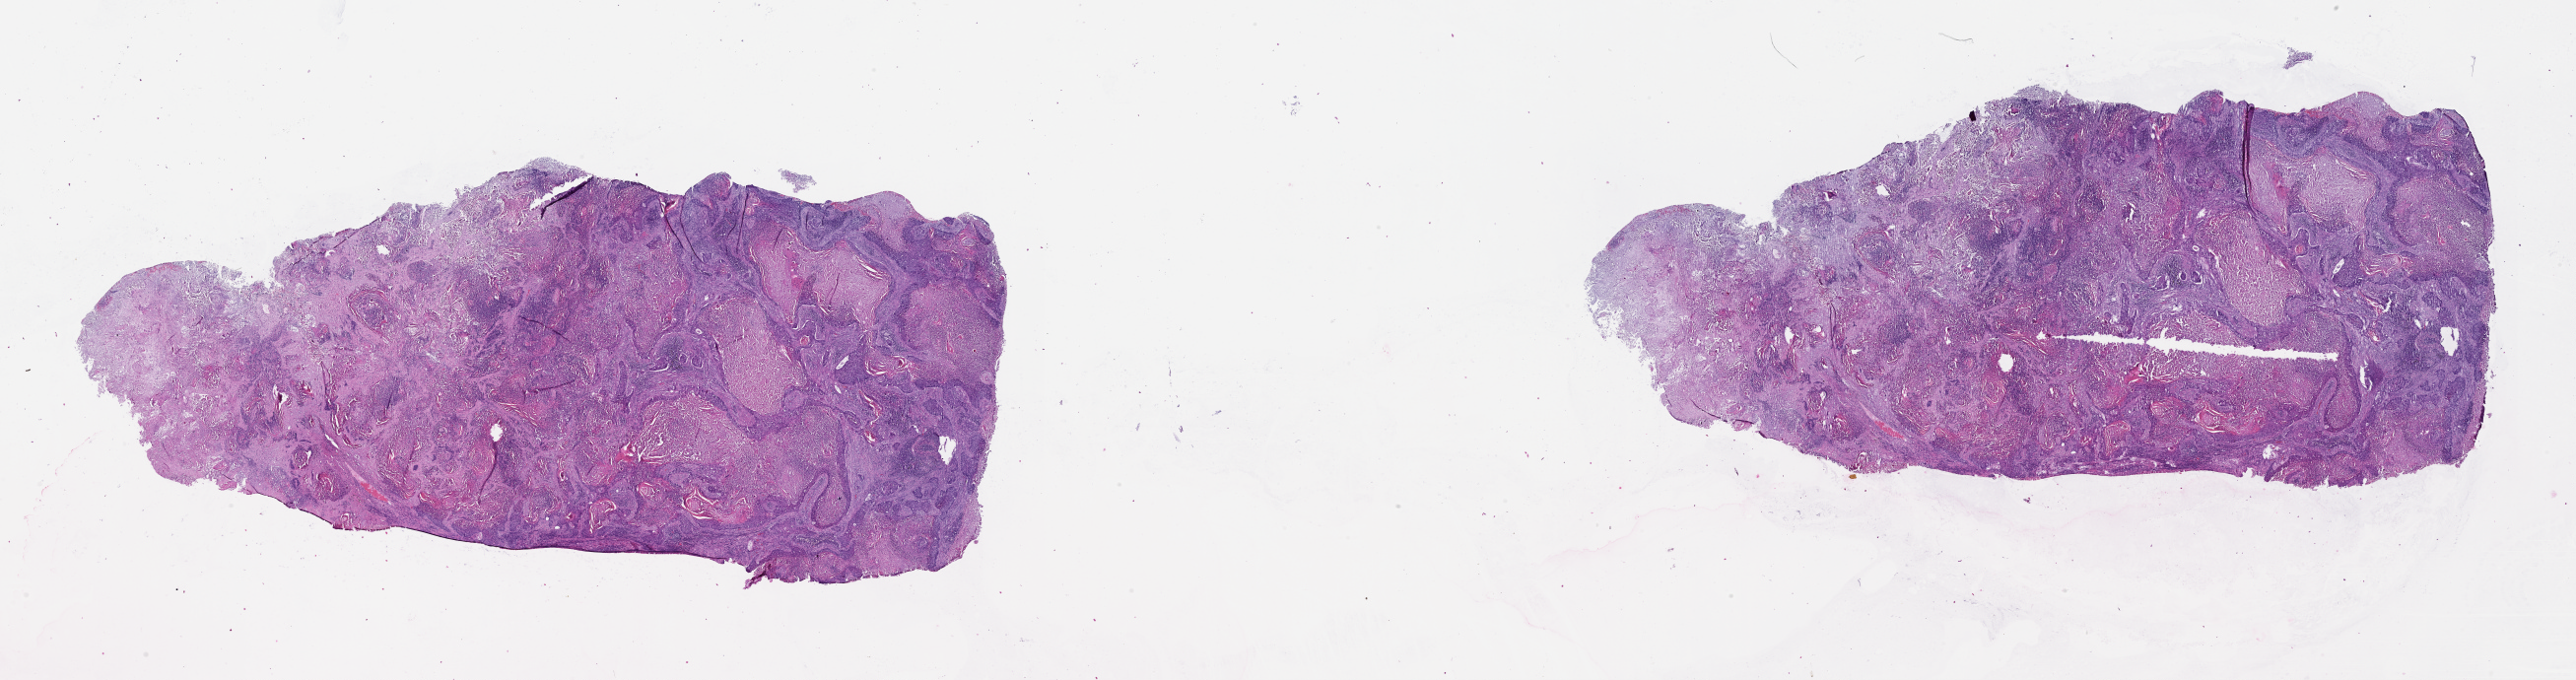
Whole-slide histology image, H&E-stained, whole scanned area (about 42.1 x 11.1 mm) shown as a low-resolution overview; tumour tissue sample, lung. Male, 49 y/o.
* patient diagnosis (cohort enrolment): squamous cell carcinoma (lung)